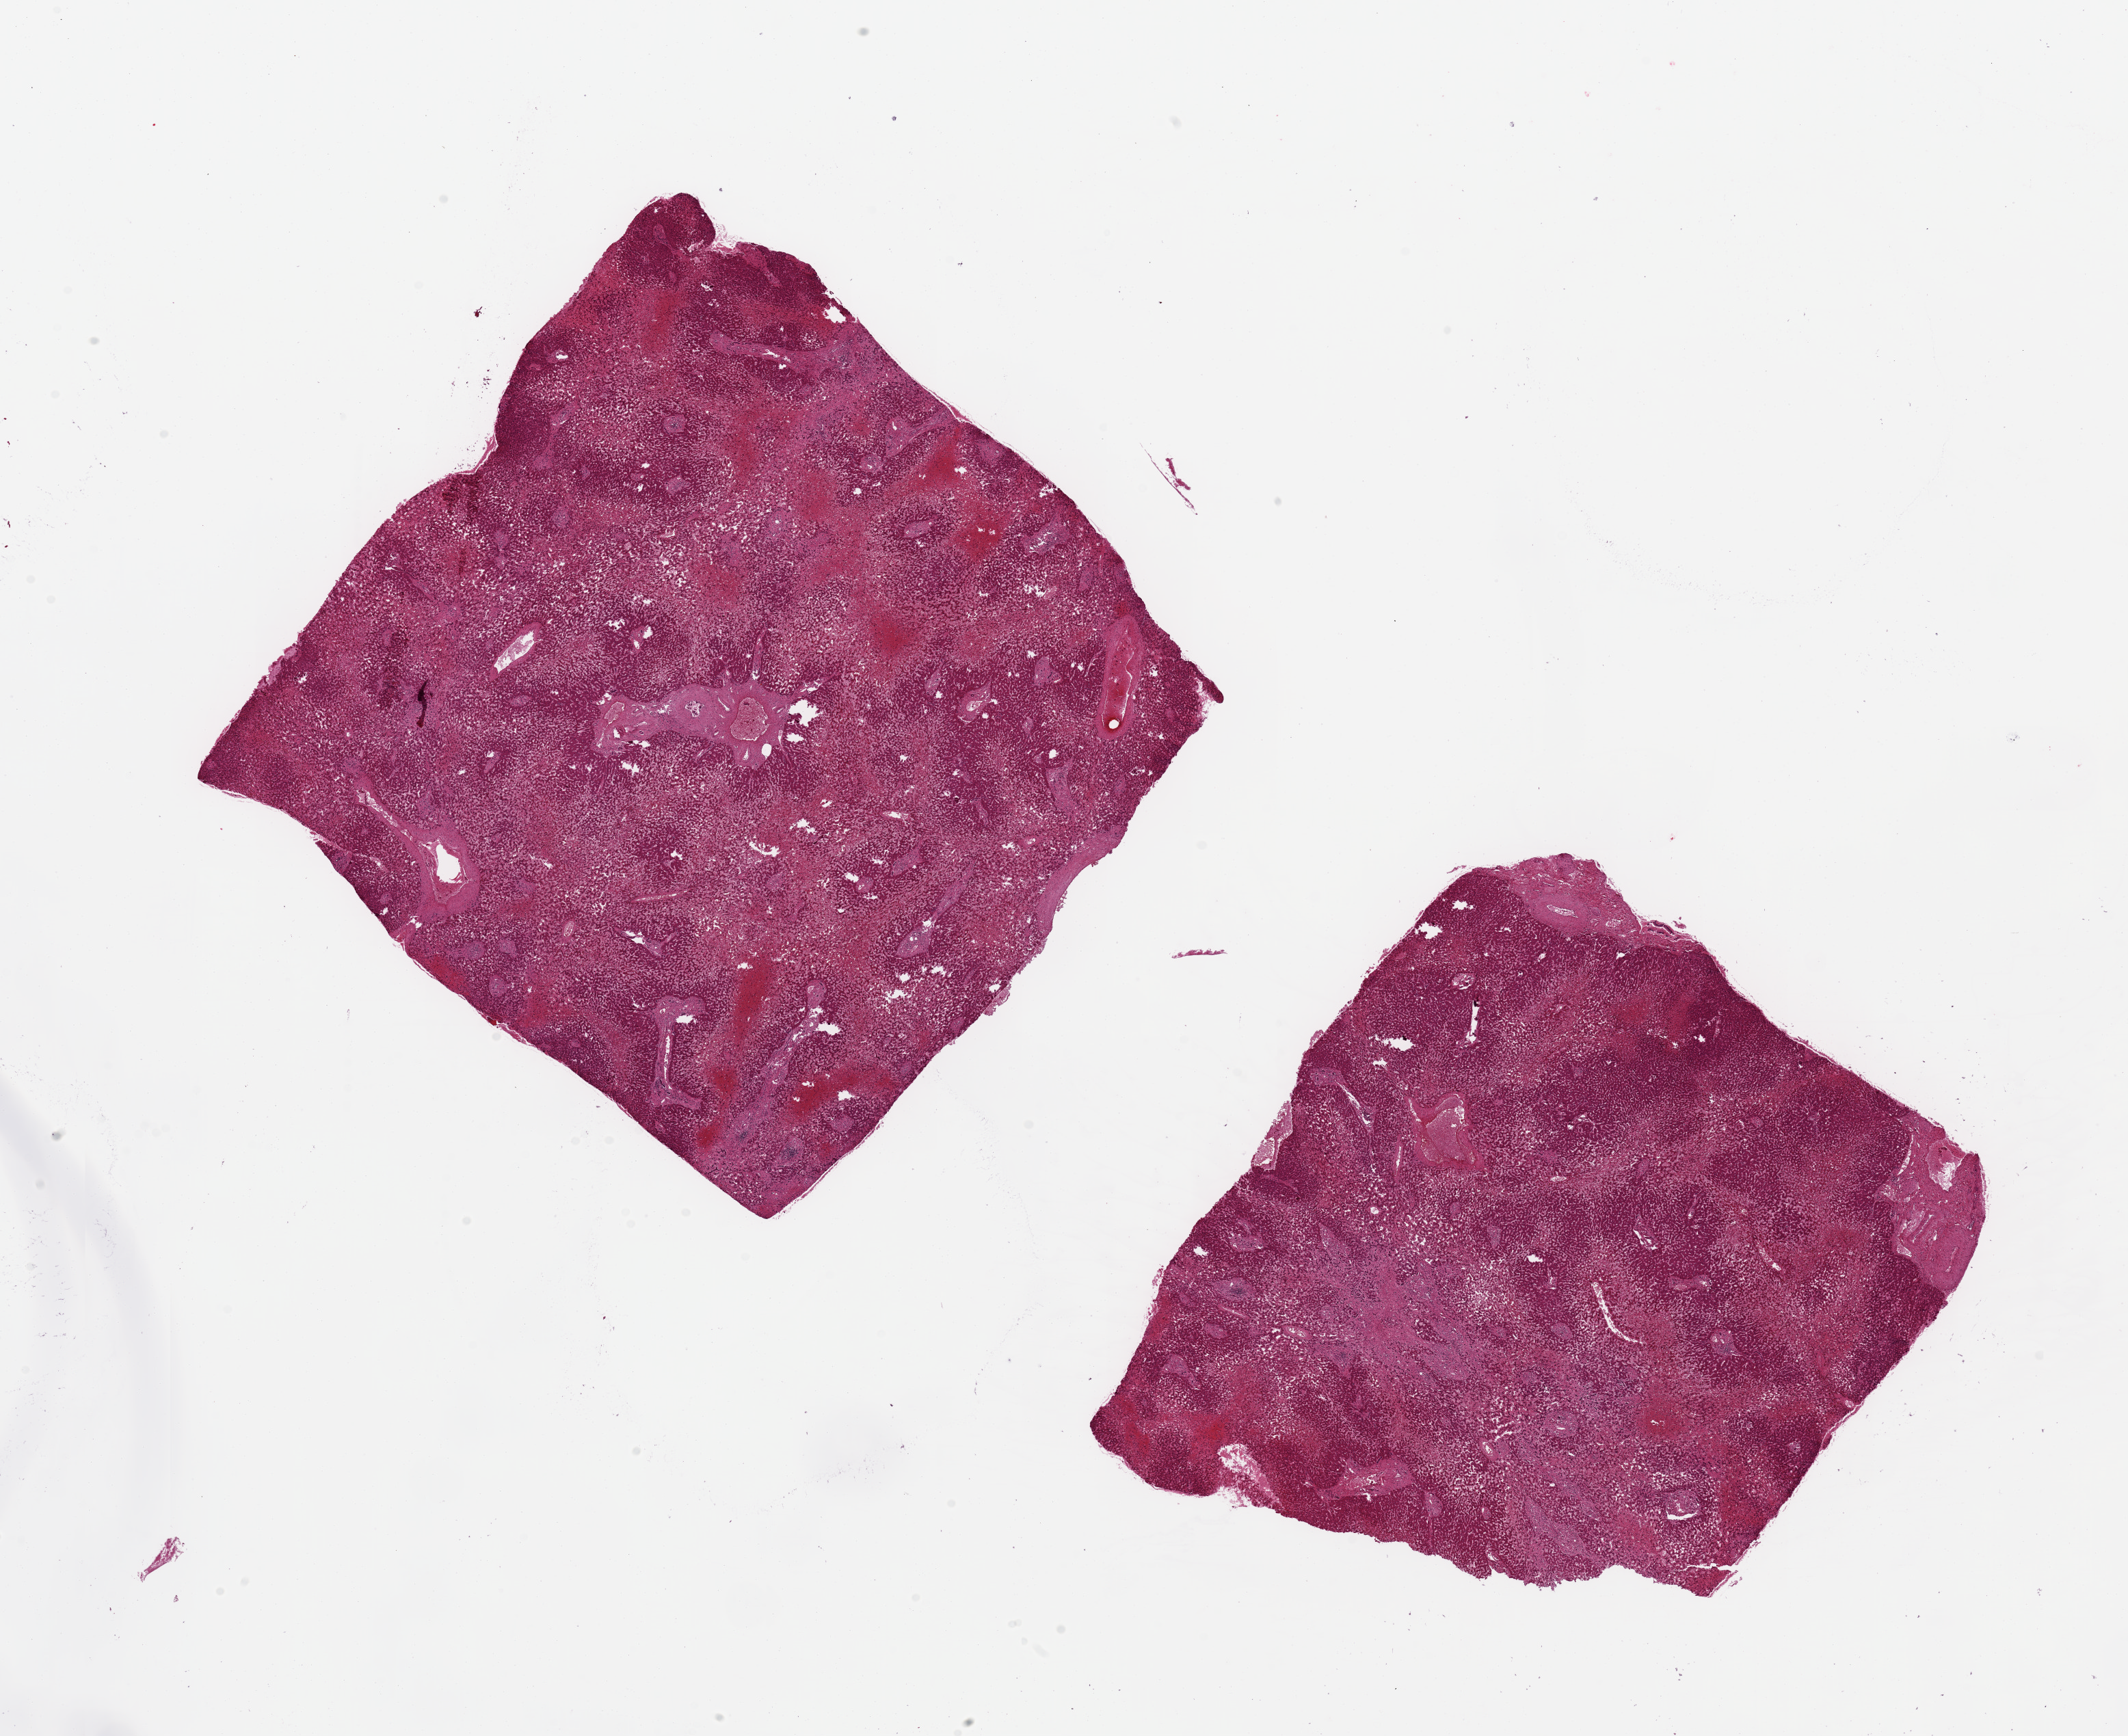
Whole-slide image, H&E stain, brightfield — a low-resolution overview of the entire scanned area, about 24.6 x 20.1 mm (slide scanned at 20x); PAXgene-fixed paraffin-embedded (PFPE) section; sampled site (target tissue): liver; donor tissue sample. Male donor.
Reviewer comment on this tissue sample: 2 ~8x7.5mm pieces. Pronounced centrilobular chronic passive congestion.